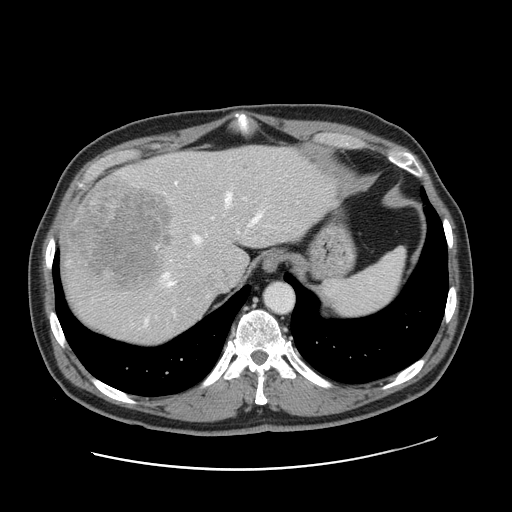
Contrast-enhanced abdominal CT, one axial slice. Position 128 of 178 along the scan axis. 120 kVp. Intravenous contrast given. Soft-tissue window (W 400 / L 40 HU). 512 × 512 image matrix, field of view 403 × 403 mm. Male patient, age 63 years. From the clinical record (not read from this slice): diagnosis: colorectal cancer liver metastases, imaged before liver resection; multiple liver metastases: yes; largest metastasis: 8 cm; disease in both lobes: yes.
Structures marked on this image (expert manual segmentation):
- hepatic veins: bounding box <164,192,260,286> (left, top, right, bottom; pixels)
- liver: <61,146,336,344>
- planned liver remnant (the part of the liver to remain after resection): <152,148,335,278>
- portal vein (with intrahepatic branches): <156,182,177,247>
- liver metastasis: <68,181,173,290>